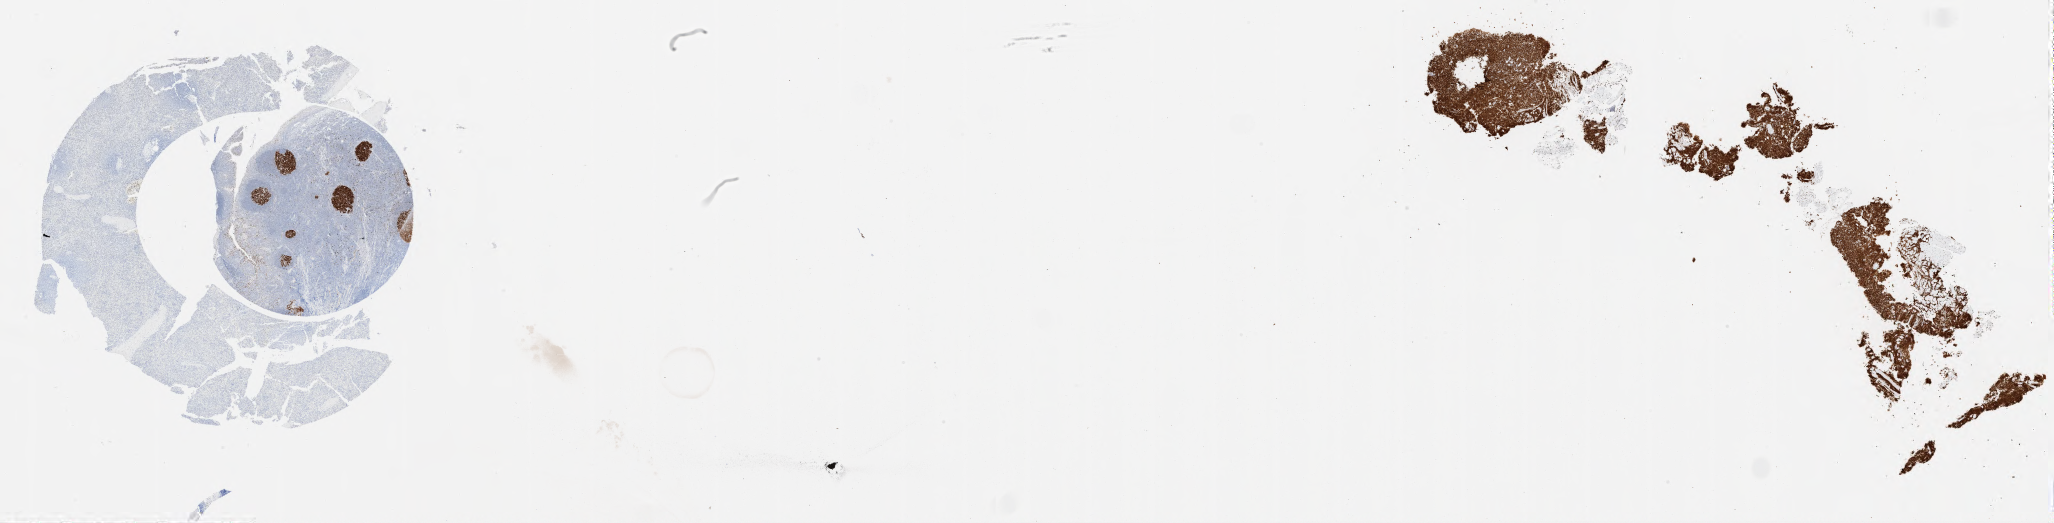
Immunohistochemistry (IHC) whole-slide image stained for BCL6 — shown as a low-resolution overview of the whole scanned area (about 33.0 x 8.4 mm); tumor tissue. Patient female; age 69 years.
* histologic diagnosis: Burkitt lymphoma, NOS